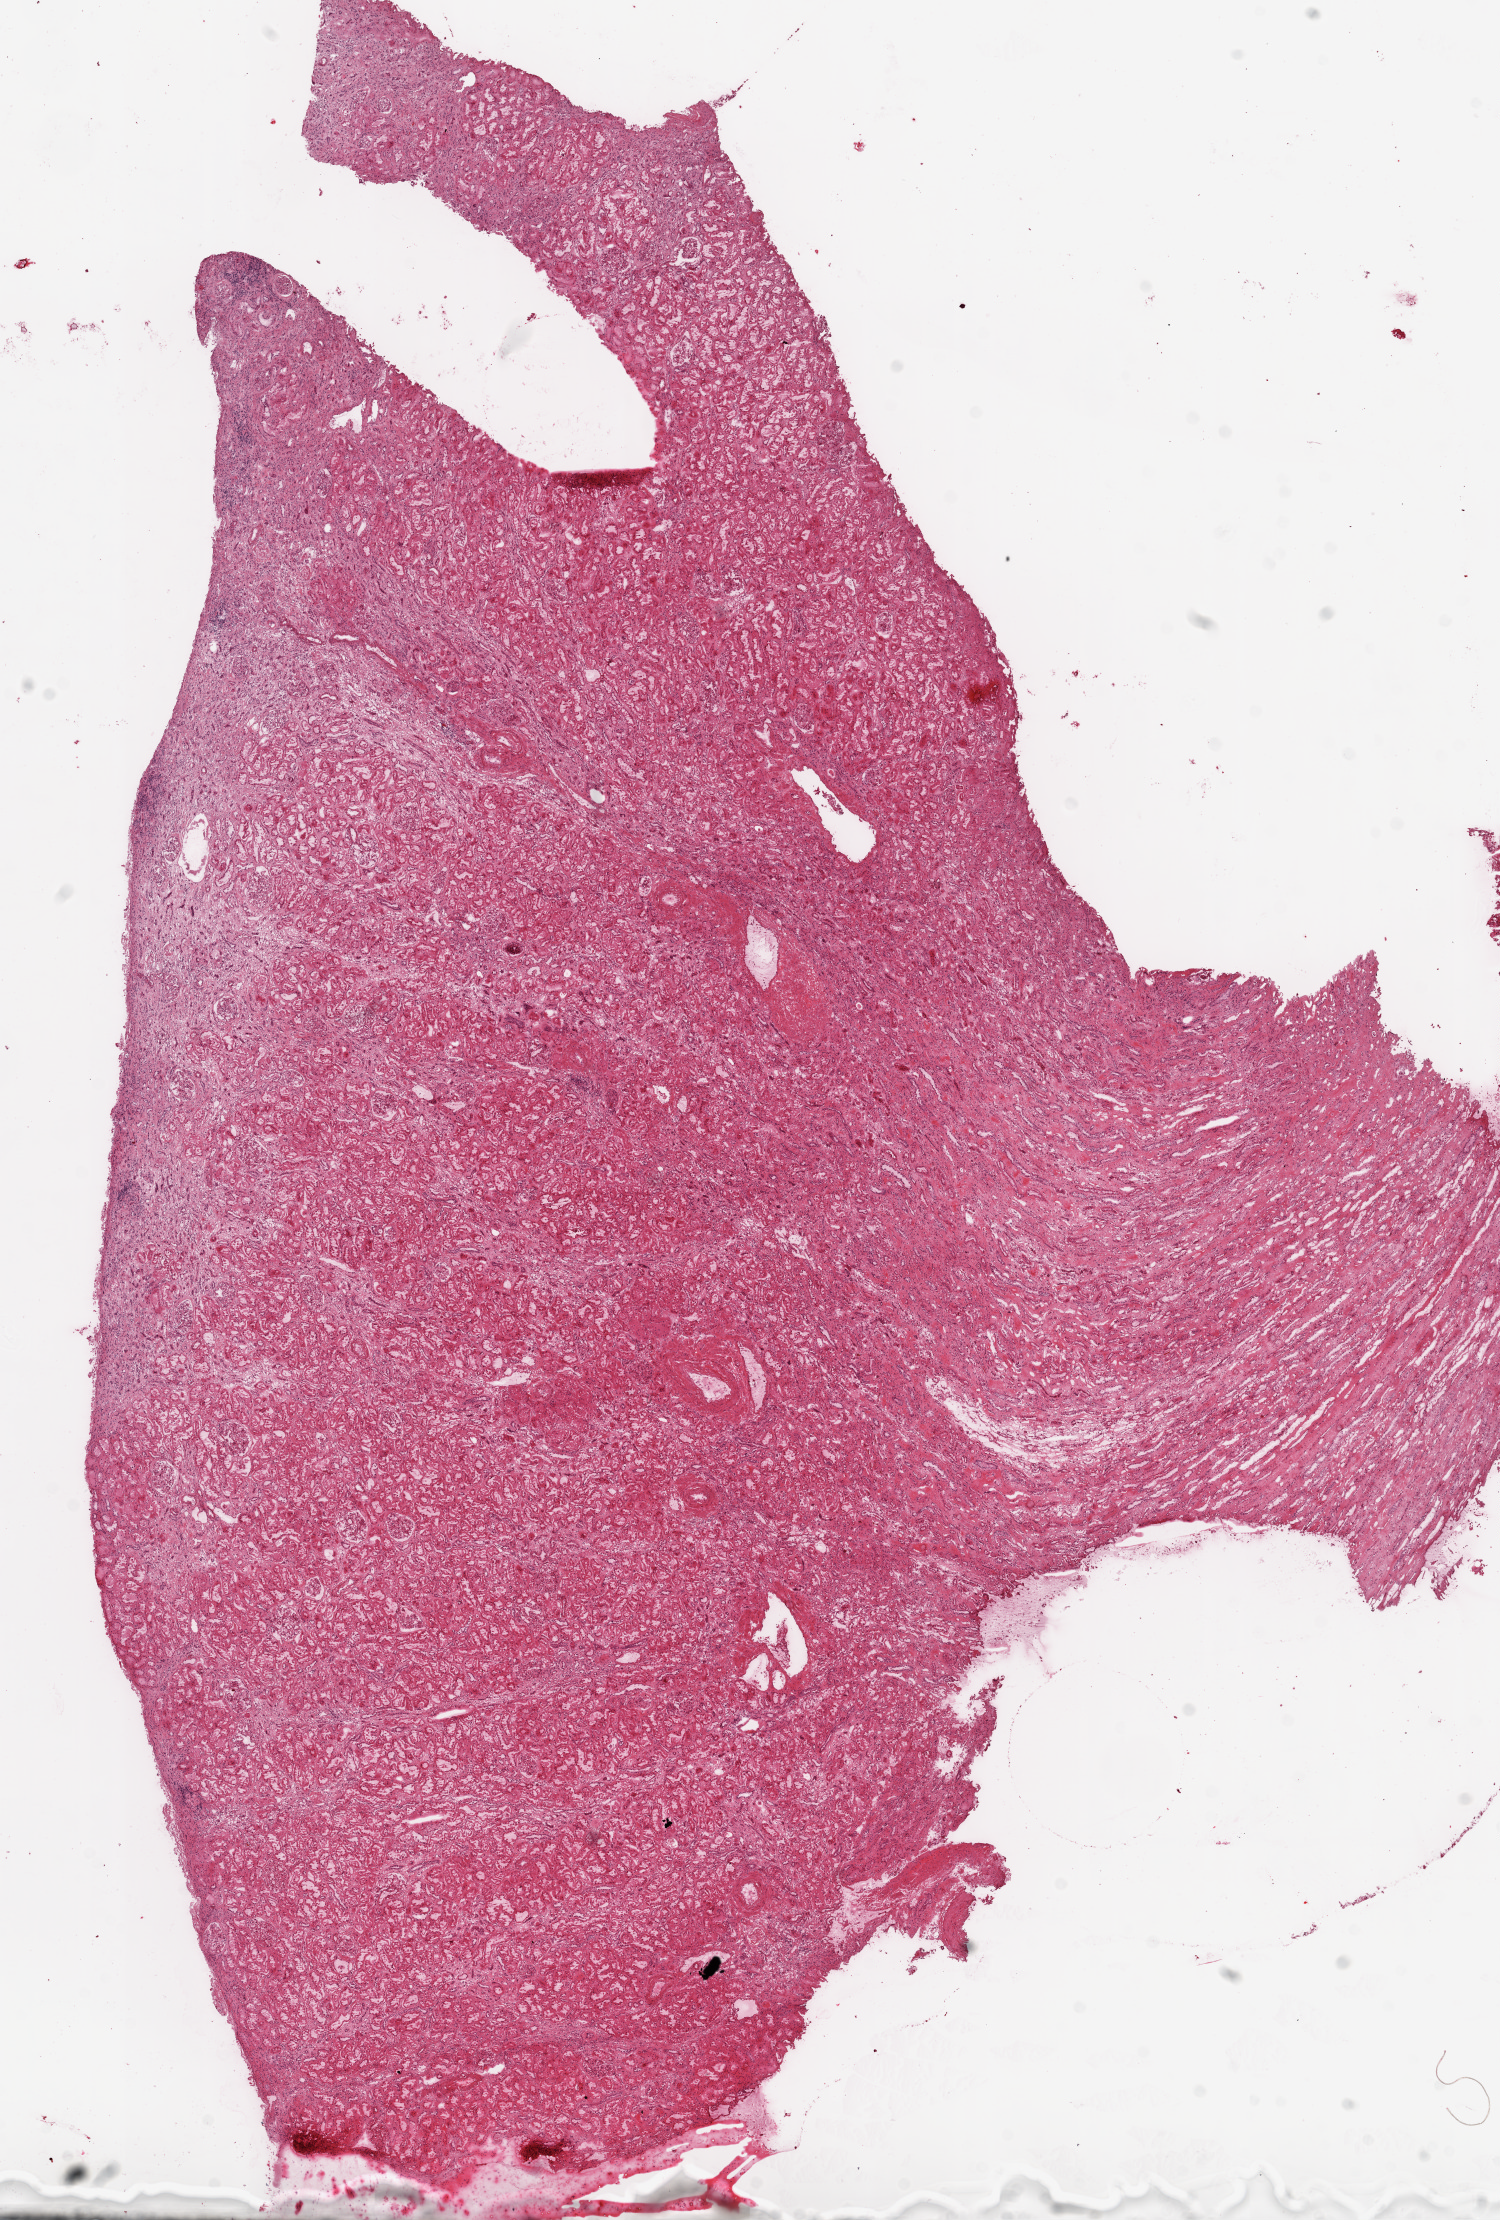
H&E-stained whole-slide image, whole scanned area (about 12.0 x 17.8 mm) shown as a low-resolution overview; frozen section; kidney, solid tissue normal (non-tumour tissue) sample. Patient: male, age at initial diagnosis 72 years.
This section: solid tissue normal sample (biorepository sample class). Patient diagnosis: Clear cell adenocarcinoma, NOS.